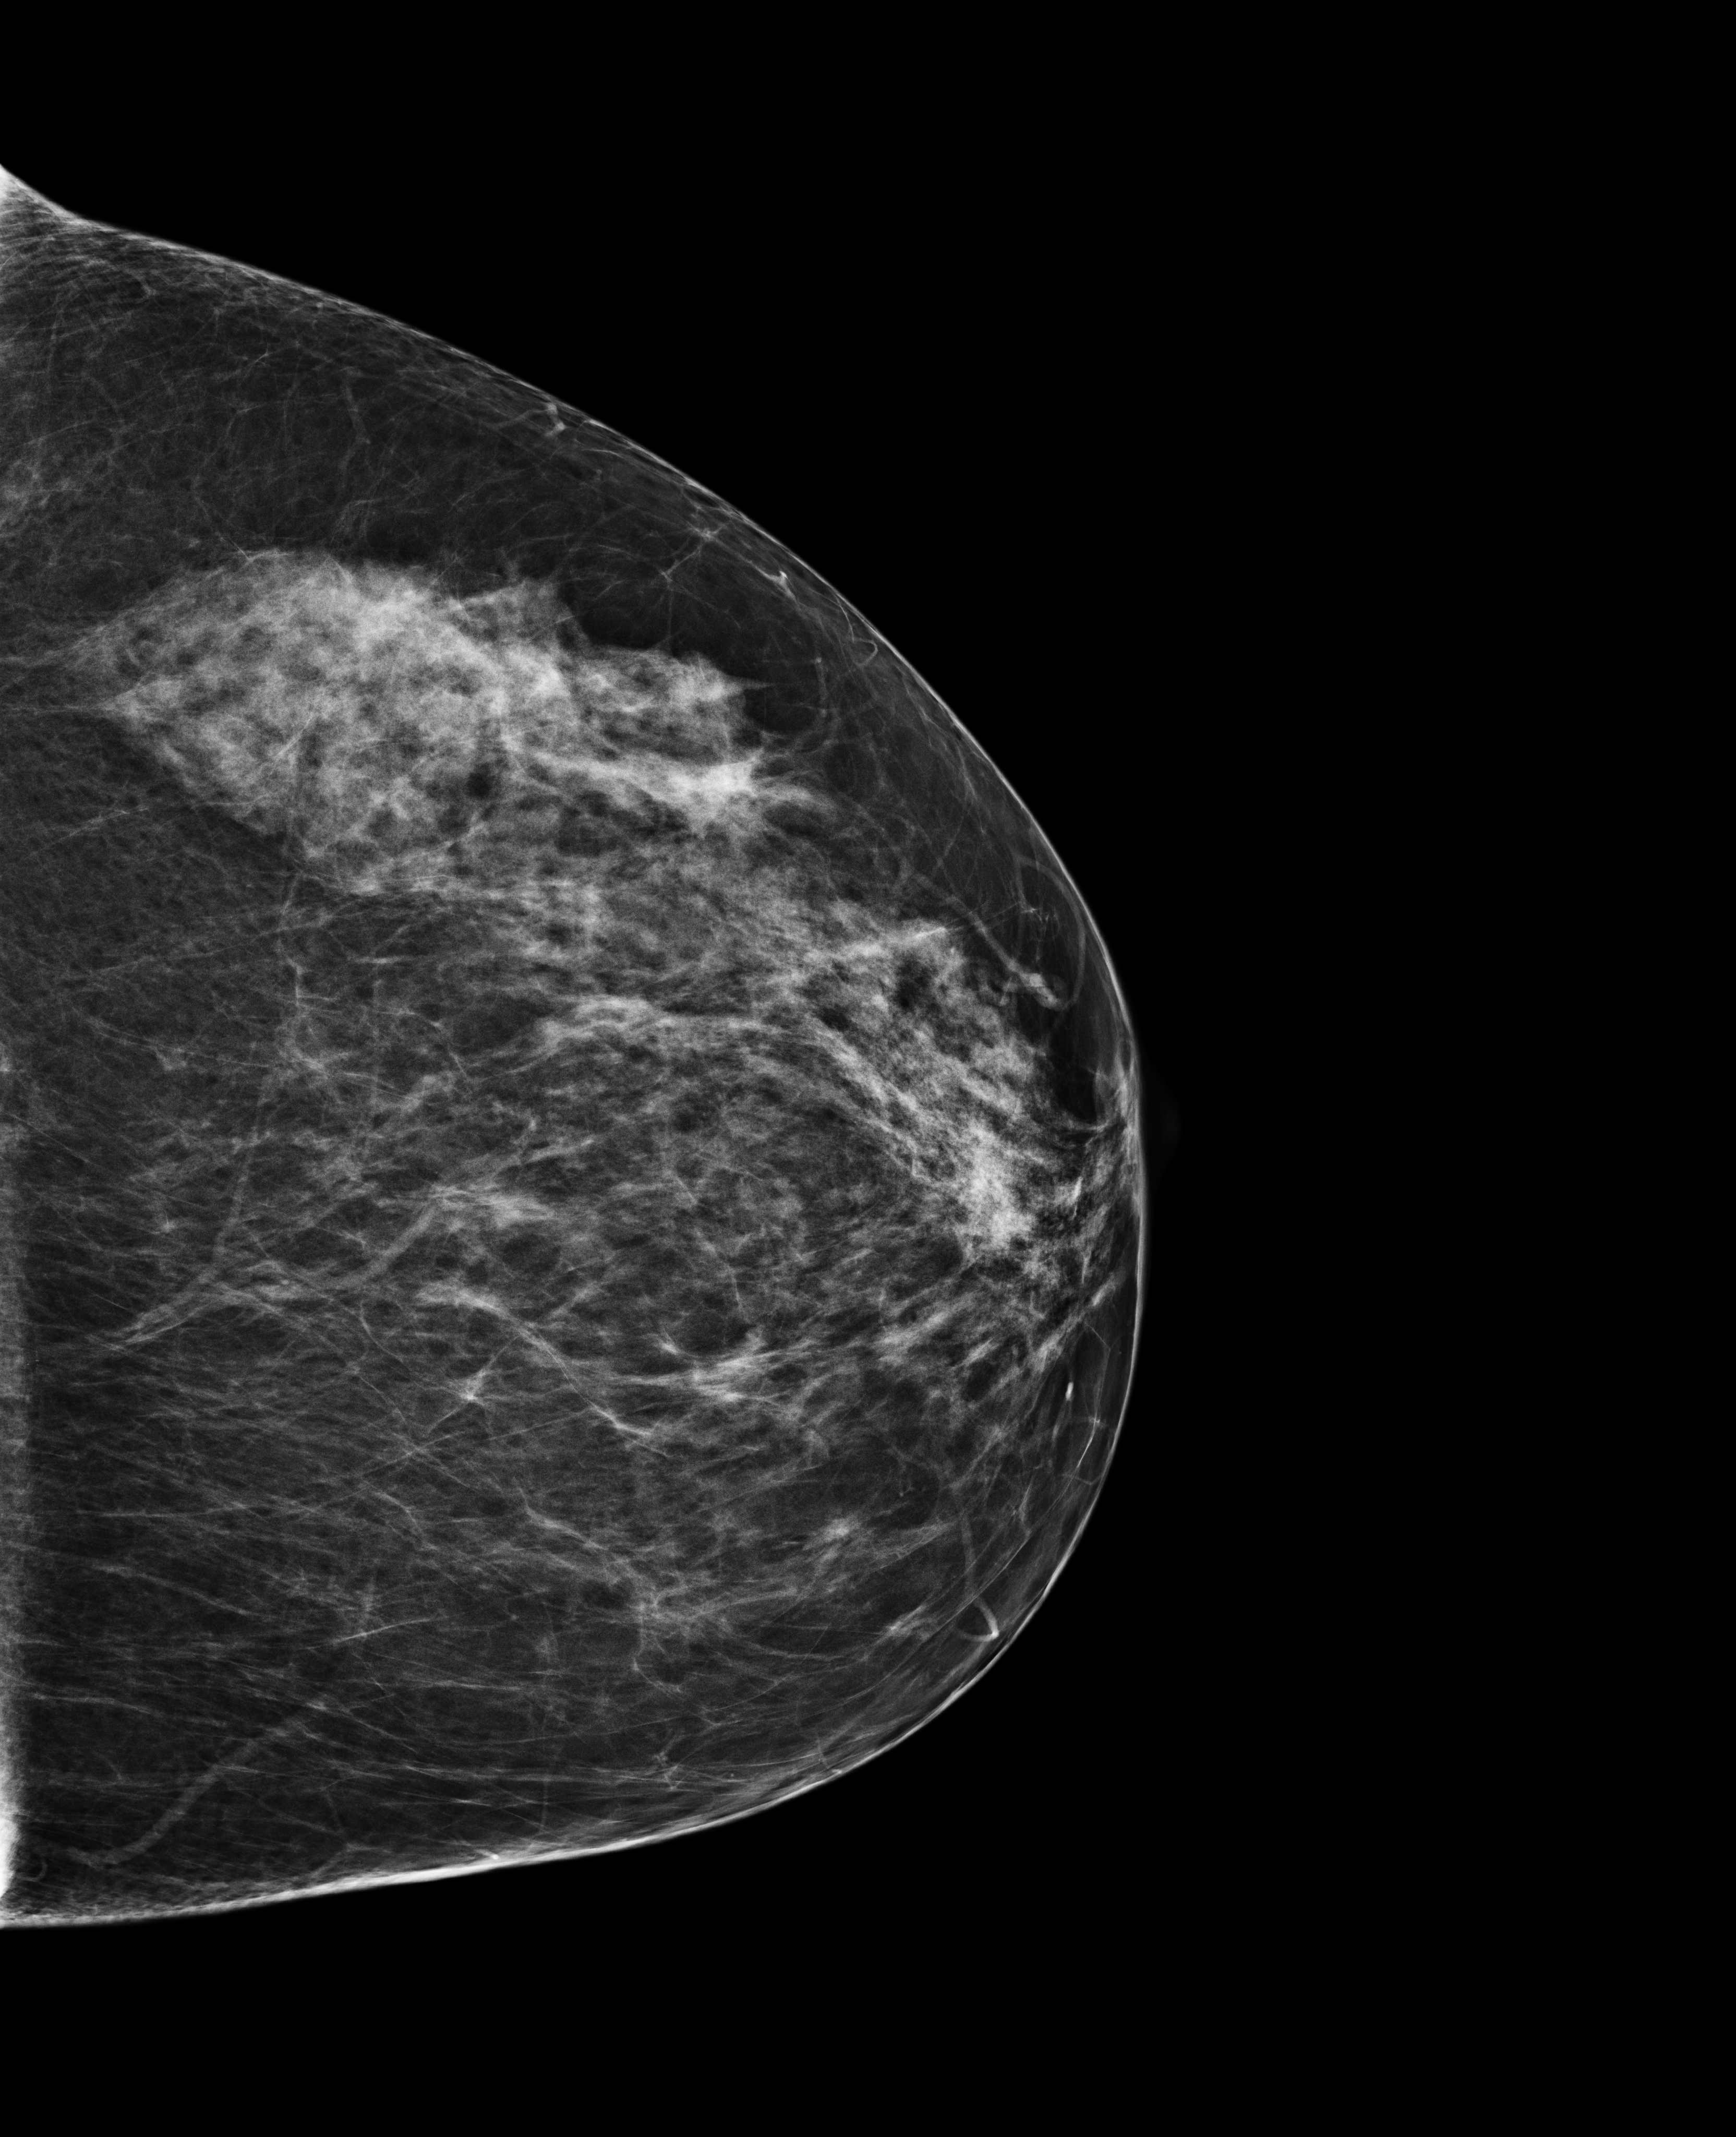
Digital mammogram (FFDM); left breast; craniocaudal (CC) view; annual screening mammography examination; system: Selenia Dimensions. Patient: female, 58 years.
Final BI-RADS category for the screening round (tomosynthesis exam, both breasts): category 1.